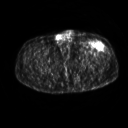
FDG PET of an extremity soft-tissue mass (from a PET/CT study), one axial slice. Position 256 of 267 along the scan axis. 3.27 mm slice thickness. 128 × 128 image matrix, field of view 500 × 500 mm. Patient: male, 64 years. Case-level facts recorded for this patient, not image findings: histological type: extraskeletal osteosarcoma; grade: high; site of the primary tumour: thigh.
Annotated regions visible in this slice (expert contour drawn on MRI and transferred to this co-registered scan by the dataset authors):
- gross tumour volume (mass): bounding box [x1, y1, x2, y2] px = [92, 42, 105, 49]